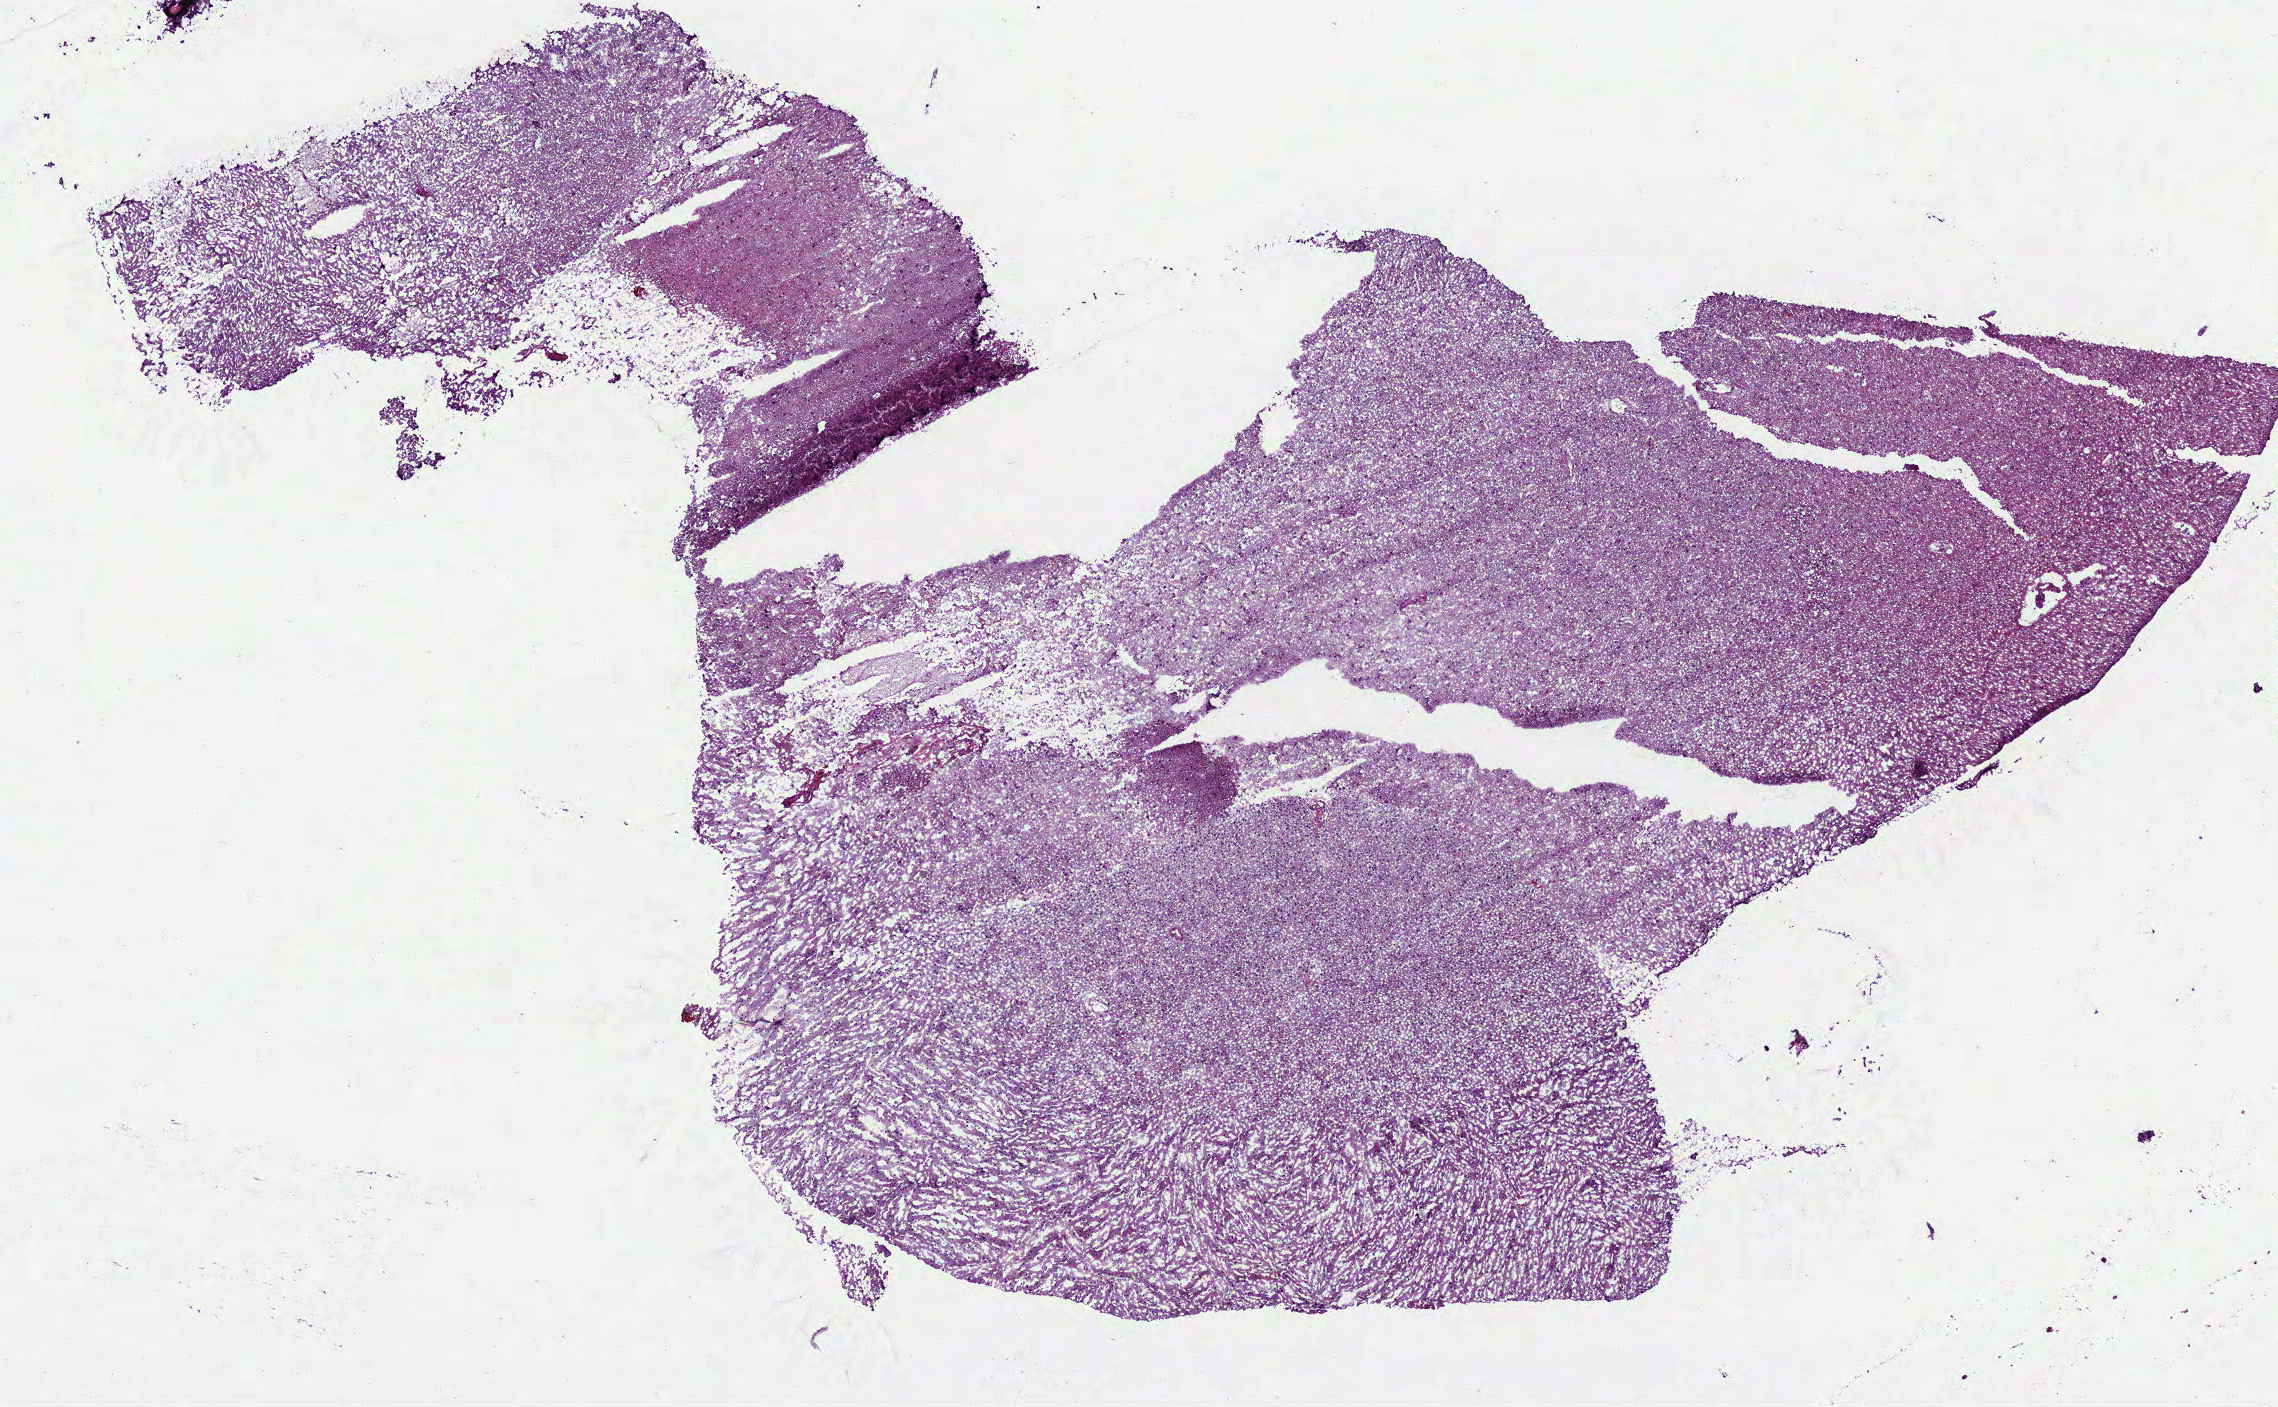
Digitized Hematoxylin and eosin (H&E) stained tissue section (whole slide) — shown as a low-resolution overview of the whole scanned area (about 9.2 x 5.7 mm, acquisition: 40x scan). Frozen section from the bottom of the tissue portion. Sample: primary tumour, brain. Female, age 41 years at initial diagnosis. Histologic grade: G3 (poorly differentiated). Slide review estimates, as recorded: tumour cells 90%, tumour nuclei 60%, normal cells 10%, stromal cells 0%, necrosis 0%.
Laterality: right. Pathologic diagnosis: Oligodendroglioma, anaplastic (cerebrum).